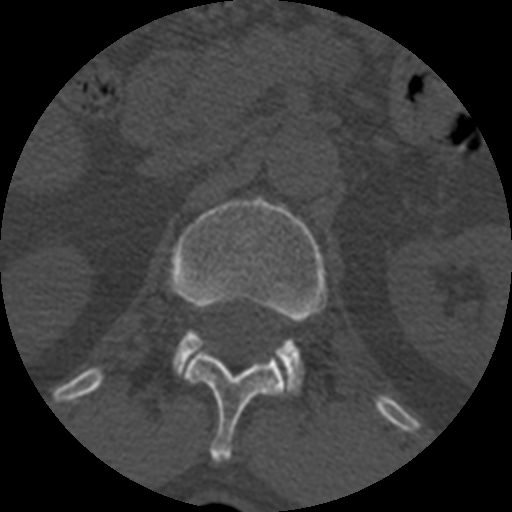
CT including the spine, one axial slice; slice 373 of 399 in the series (ordered by position); reconstruction kernel STANDARD; 120 kVp; bone window (W 1800 / L 400 HU); 512 × 512 image matrix, field of view 160 × 160 mm. Patient age 71 years. Case-level facts recorded for this patient, not image findings: primary cancer: prostate.
Outlined on this slice (semi-automatically segmented with operator editing):
- L1 vertebra: bounding box [x1, y1, x2, y2] px = [170, 199, 326, 396]
- T12 vertebra: [183, 349, 288, 462]